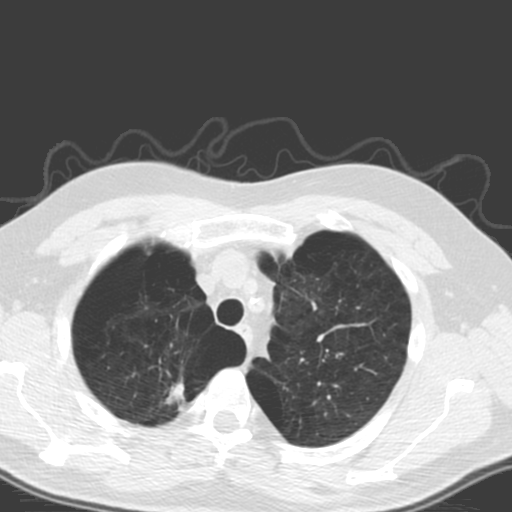
Low-dose screening chest CT, axial slice; first (baseline) screen; lung window (W 1500 / L -600 HU); 3.2 mm slice thickness; standard (soft-tissue) reconstruction kernel (B); 120 kVp; slice 34 of 173 in the series; 512 × 512 image matrix, field of view 340 × 340 mm. Male, age 56 years at enrolment. Former smoker at enrolment.
• Expert reader's lesion annotation, bounding box (x1, y1, x2, y2) in pixels: (141, 354, 209, 432).
• Reader record for this screening exam (exam-level; its link to the box is not recorded): non-calcified nodule or mass ≥4 mm, right upper lobe, 20 × 12 mm, spiculated (stellate) margins, soft tissue attenuation.
• Later outcome: lung cancer diagnosed 205 days after this screen — large cell carcinoma, NOS, right upper lobe, poorly differentiated (G3), stage IA (AJCC 6th edition), 18 mm at pathology.